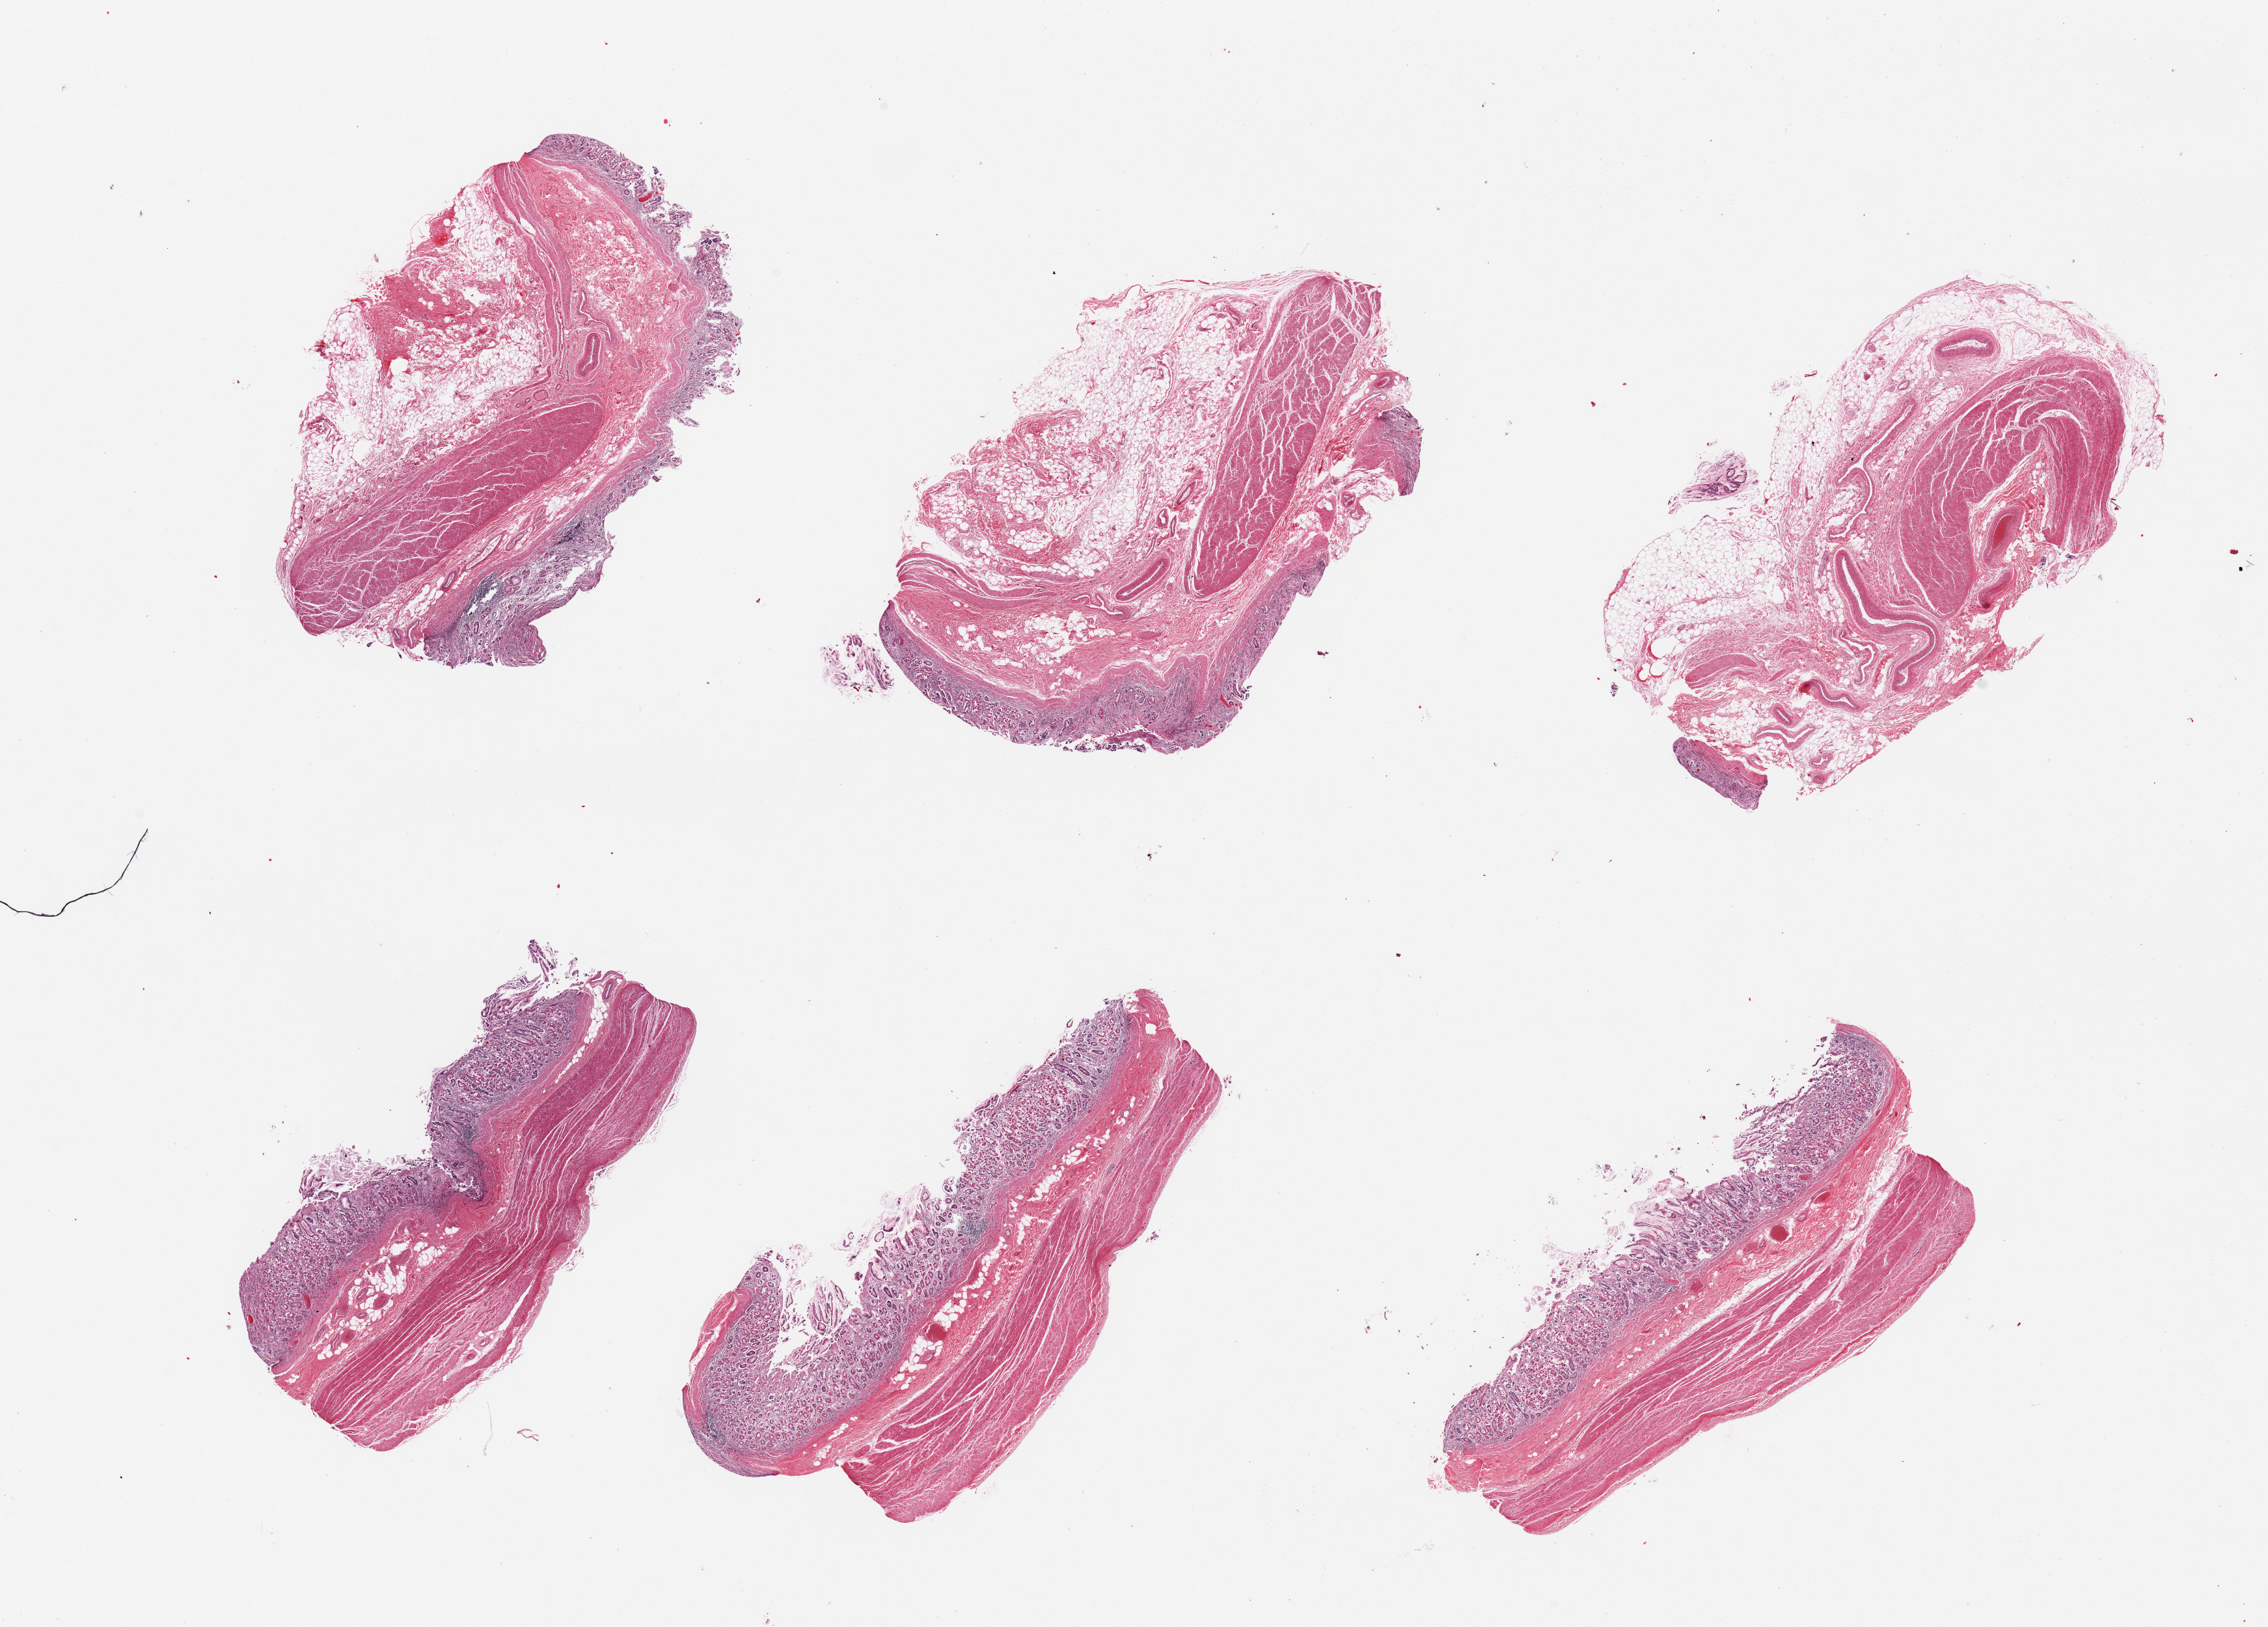
Whole-slide image, H&E stain, shown as a low-resolution overview of the whole scanned area (about 27.6 x 19.8 mm, acquisition: 20x scan); PAXgene-fixed, paraffin-embedded tissue; target tissue: stomach; tissue donor sample.
* review note (as recorded): 6 pieces; mucosa ~25-30% thickness but badly autolyzed